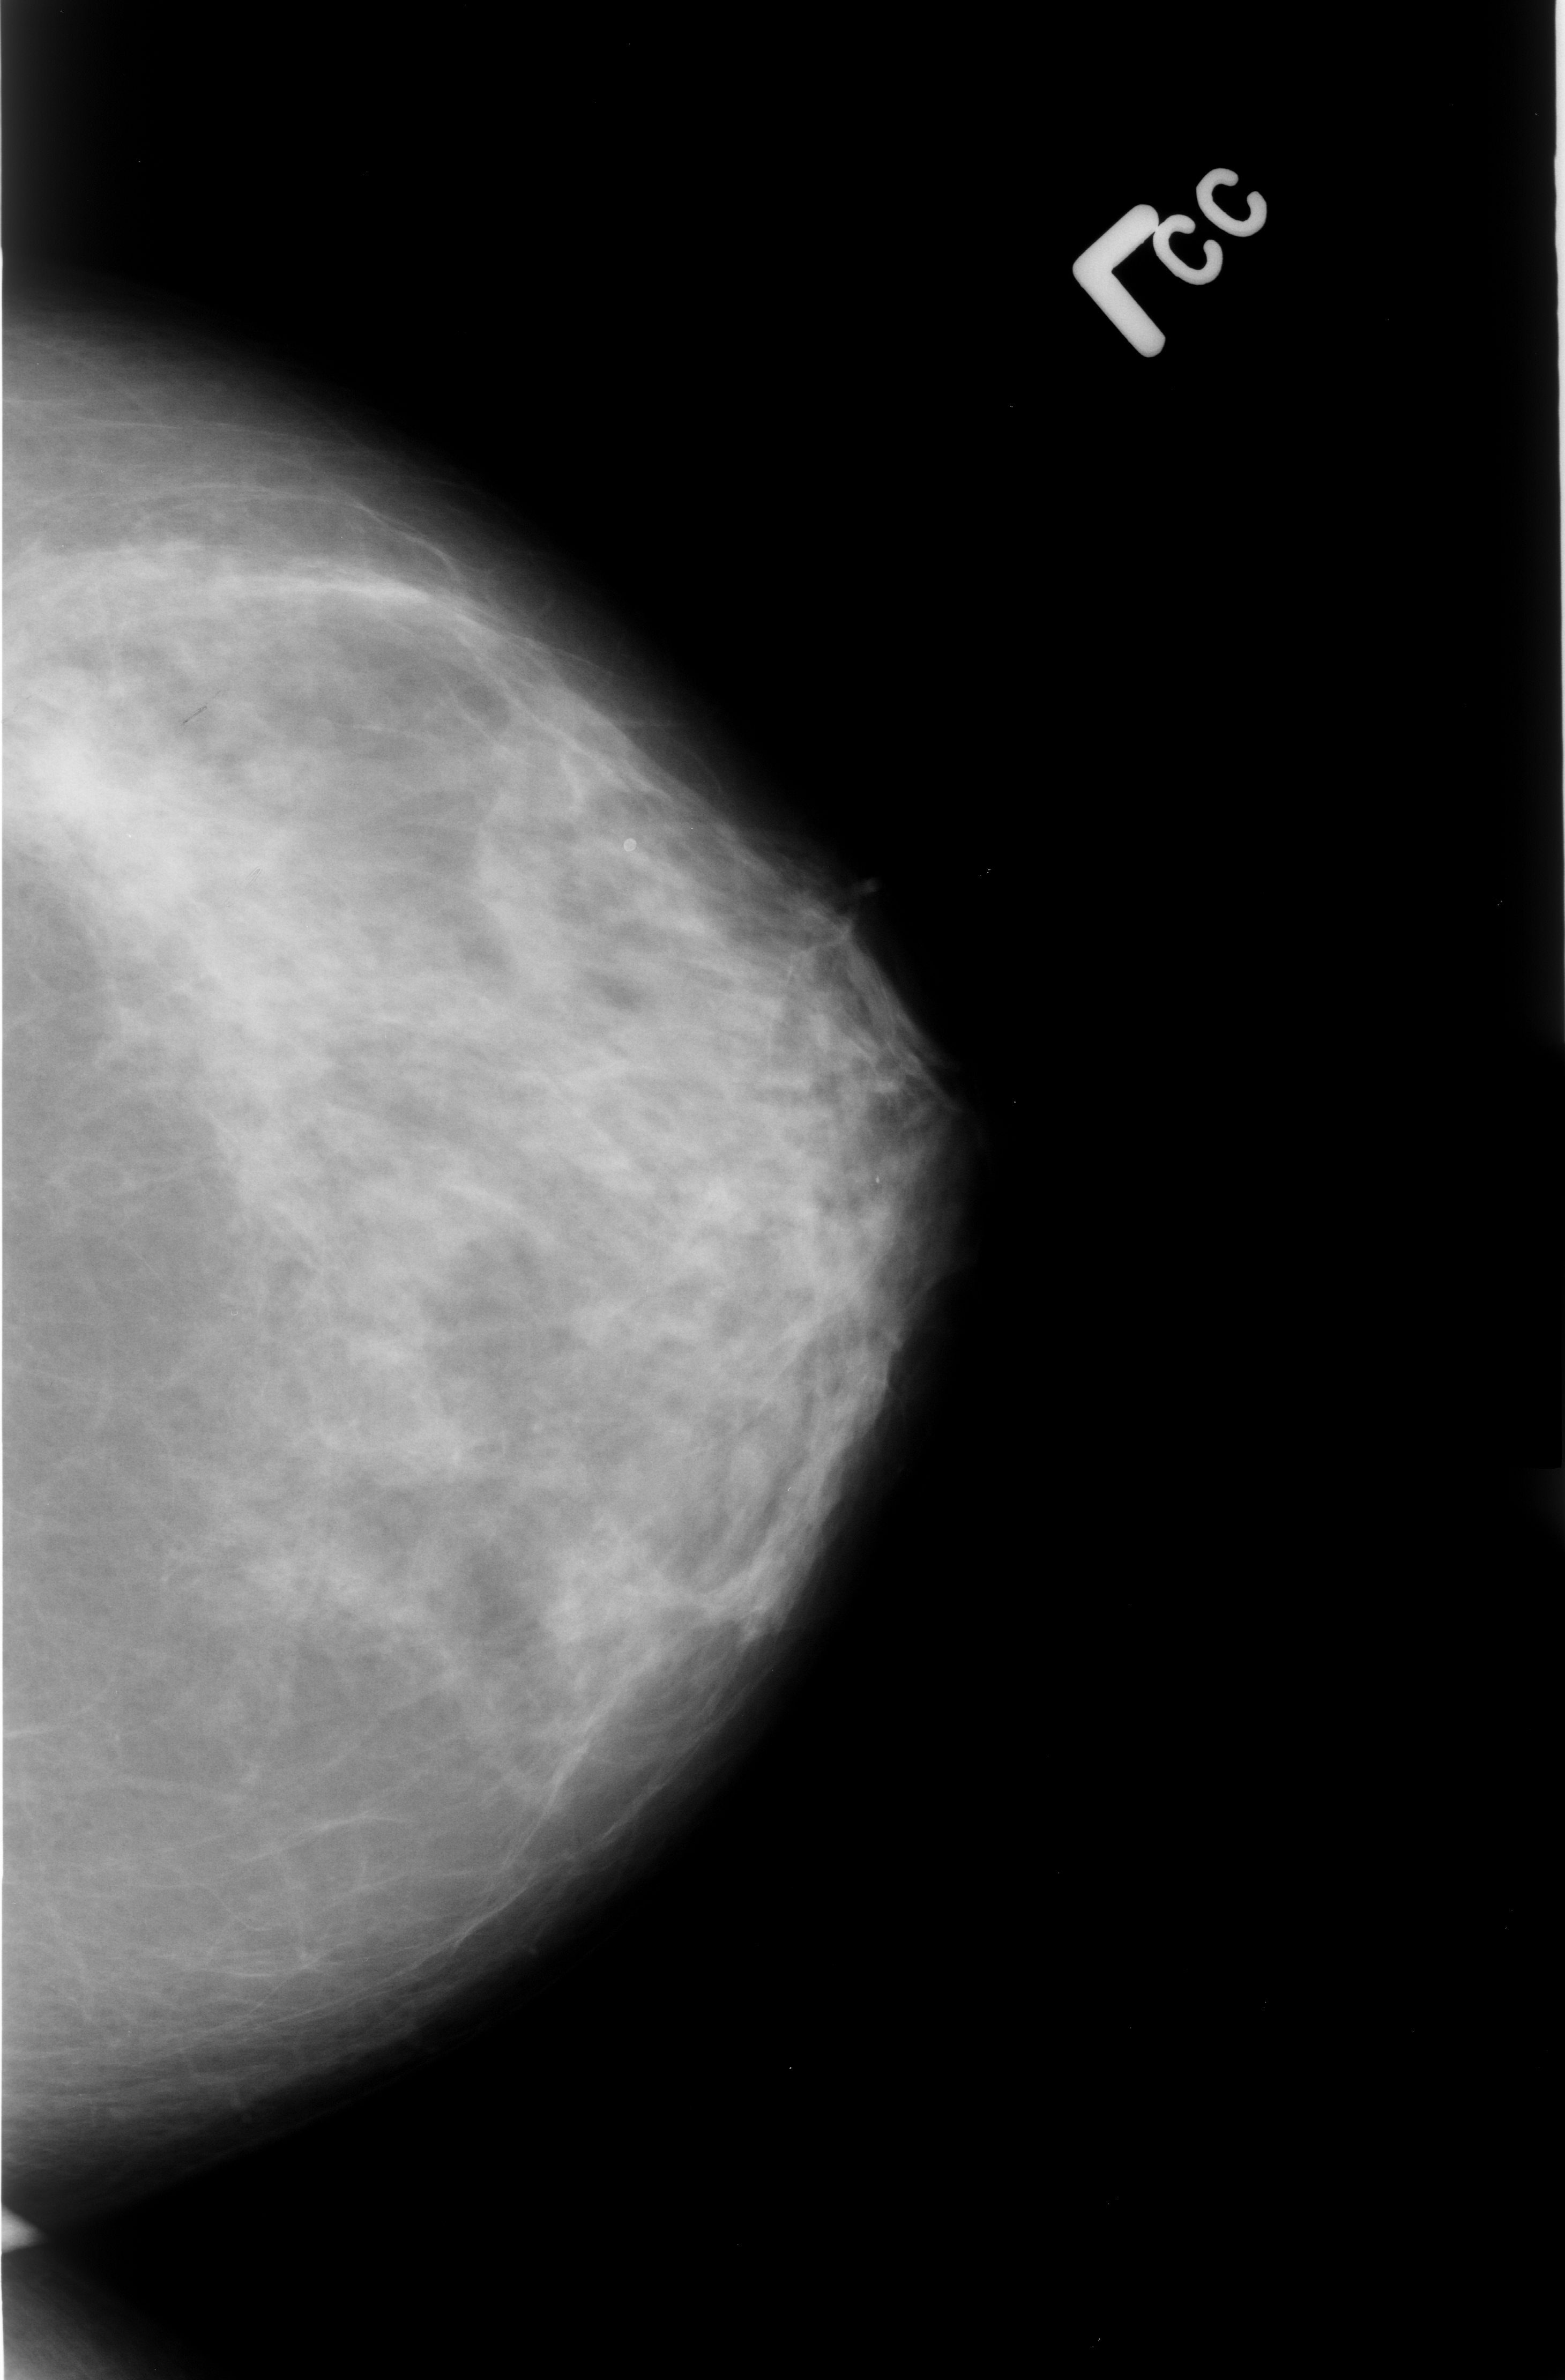
Scanned film-screen mammogram, left breast, craniocaudal (CC) view, BI-RADS breast density category 3 (scale 1–4).
Abnormality record for this image: mass, shape irregular / architectural distortion, margins ill defined / spiculated; BI-RADS assessment category 4; pathology result (as recorded, not read from the image): malignant.